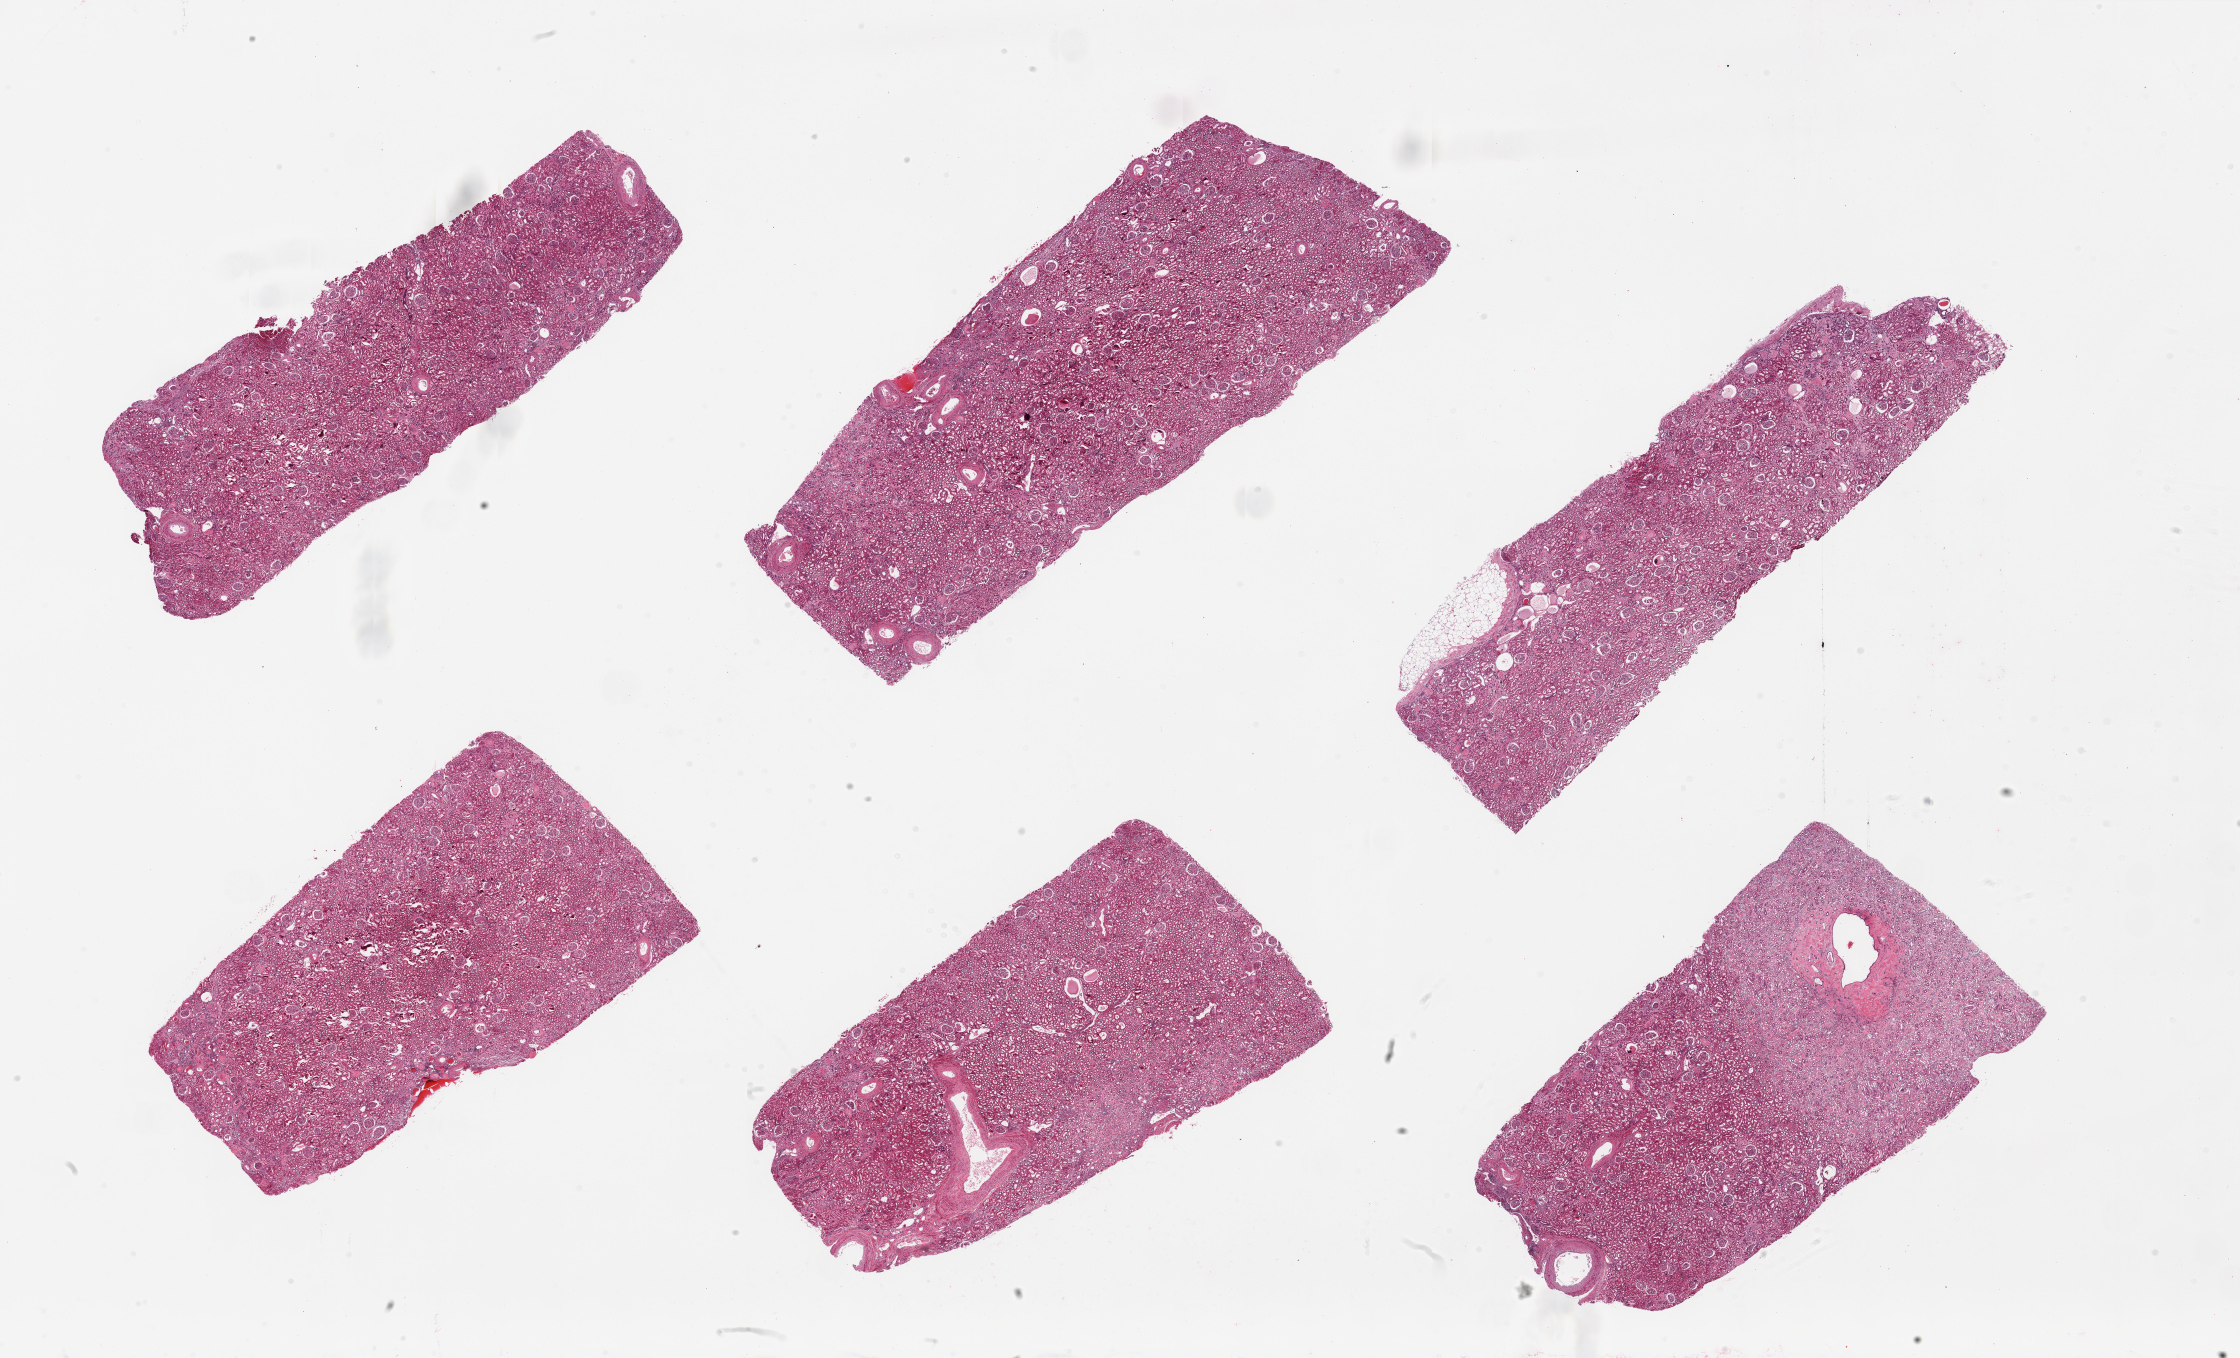
Digitized haematoxylin and eosin-stained section, low-resolution overview of the scanned area, about 35.4 x 21.5 mm (acquisition: 20x scan). PAXgene-fixed, paraffin-embedded tissue. Sampled site (target tissue): renal cortex. Tissue donor sample.
Review note (as recorded): 6 pieces; admixture with medulla in 2 pieces; no chronic lesions except for medullary hyalin casts in one piece.